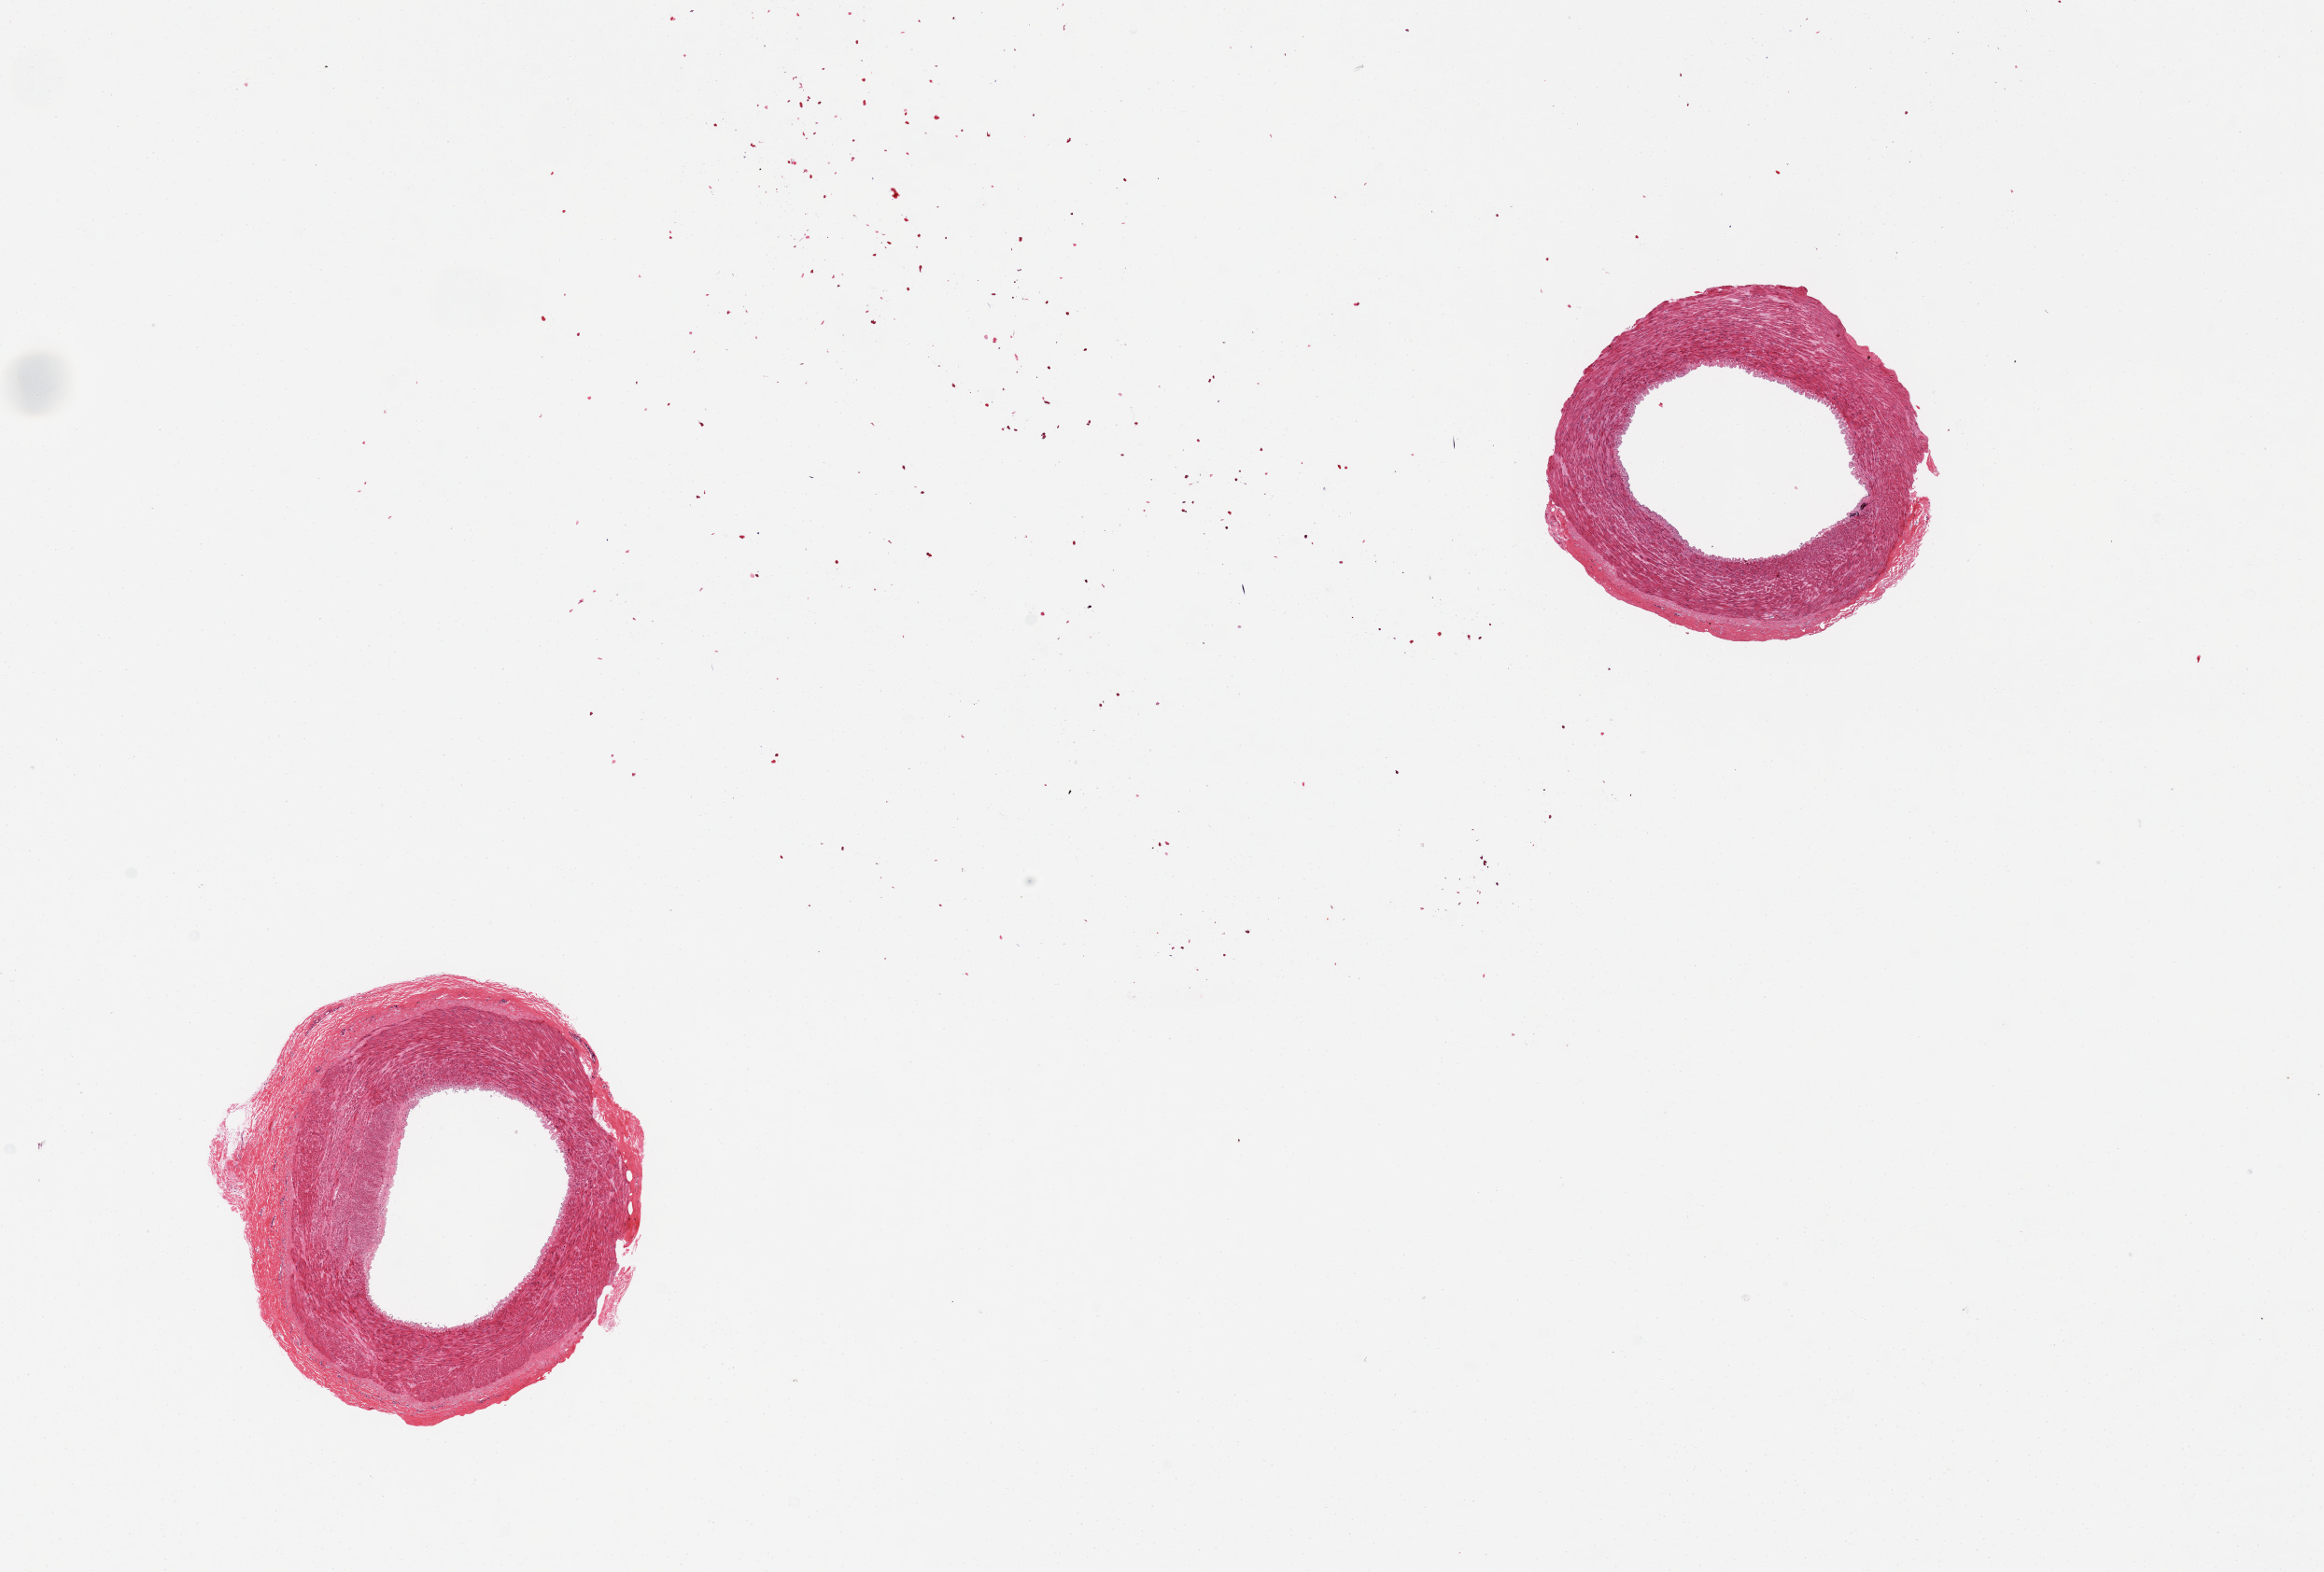
Digitized haematoxylin and eosin-stained section — shown as a low-resolution overview of the whole scanned area (about 19.7 x 13.3 mm). PAXgene-fixed, paraffin-embedded tissue. Target tissue: tibial artery. Donor tissue sample.
Review note (as recorded): 2 pieces.